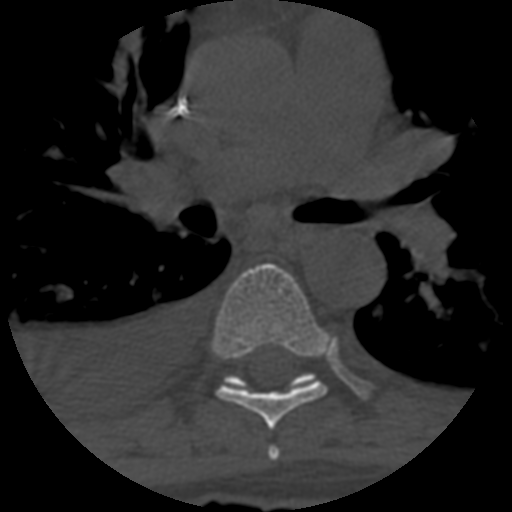
CT including the spine, one axial slice; slice 432 of 708 in the series (ordered by position); reconstruction kernel STANDARD; one of 3 acquisitions stored at this slice position; bone window (W 1800 / L 400 HU); 512 × 512 image matrix. Patient age 55 years. Case-level facts recorded for this patient, not image findings: primary cancer: colon; vertebrae with lytic lesions (as recorded): T12, L1, L5.
Outlined on this slice (semi-automatic segmentation, software-assisted and operator-edited):
- T5 vertebra: bounding box [x1, y1, x2, y2] px = [267, 446, 280, 460]
- T6 vertebra: [214, 263, 326, 430]
- T7 vertebra: [225, 375, 313, 385]